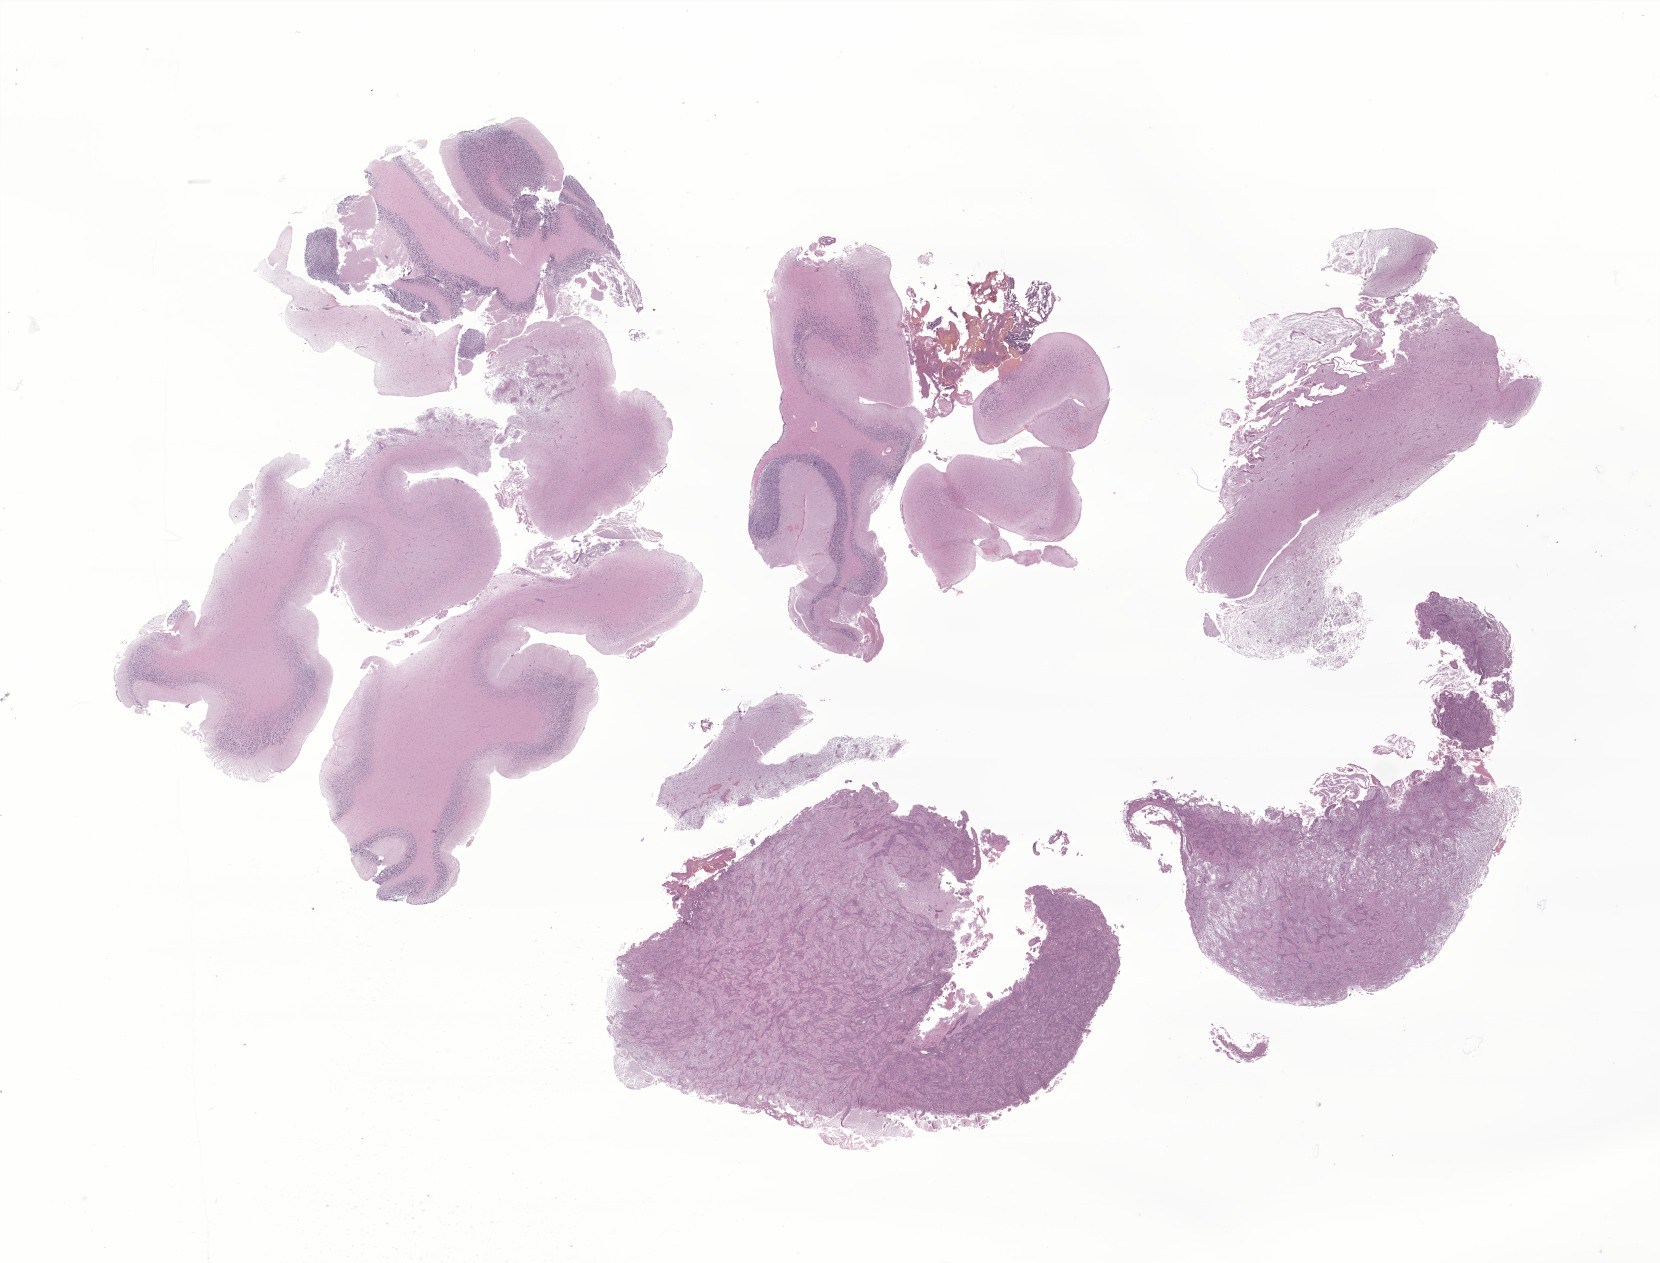
H&E whole-slide image of tumor tissue from the cerebellum, a low-resolution overview of the entire scanned area, about 28.0 x 21.3 mm. Formalin-fixed paraffin-embedded section. Female patient, age 705 days (about 1.9 years).
Diagnosis (ICD-O-3 morphology term): Glioma, malignant.